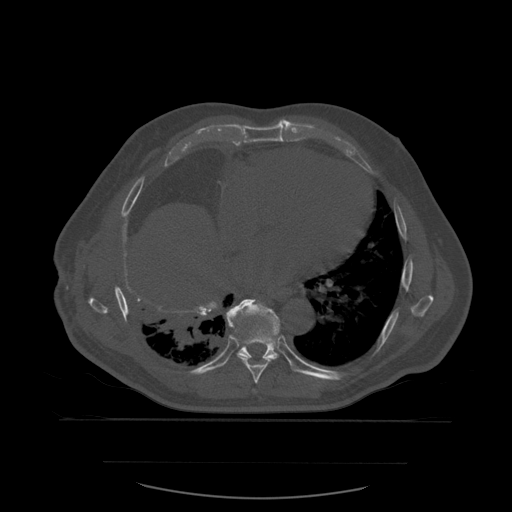
CT including the spine, one axial slice; slice 352 of 590 in the series (ordered by position); bone window (W 1800 / L 400 HU); 512 × 512 image matrix. Patient age 71 years. From the clinical record (not read from this slice): primary cancer: lung.
Annotated regions visible in this slice (semi-automatic segmentation, software-assisted and operator-edited):
- T8 vertebra: box from (x=226, y=301) to (x=279, y=384) px
- T9 vertebra: (x=224, y=299)–(x=281, y=365)